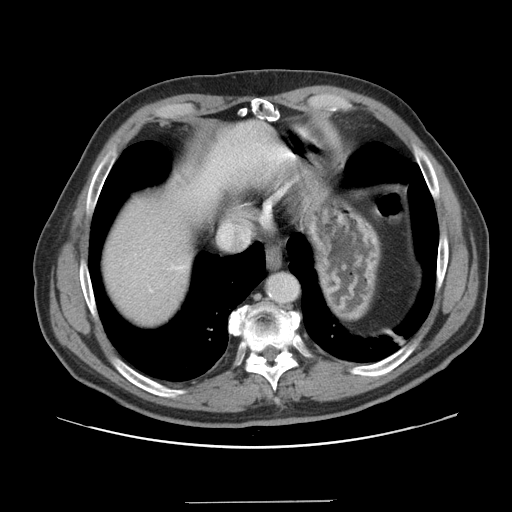
Contrast-enhanced abdominal CT, one axial slice. Position 139 of 151 along the scan axis. Intravenous contrast given. Soft-tissue window (W 400 / L 40 HU). 512 × 512 image matrix. Male patient, age 63 years. Case-level facts recorded for this patient, not image findings: diagnosis: colorectal cancer liver metastases, imaged before liver resection; multiple liver metastases: no; largest metastasis: 2.1 cm; chemotherapy before resection: no.
Outlined on this slice (expert manual segmentation):
- hepatic veins: bounding box (x1, y1, x2, y2) in pixels: (222, 235, 226, 240)
- liver: (100, 121, 290, 328)
- planned liver remnant (the part of the liver to remain after resection): (100, 160, 223, 329)